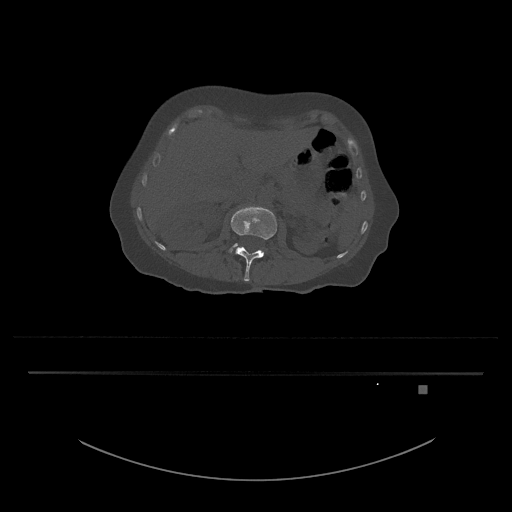
CT including the spine, one axial slice; slice 481 of 797 in the series (ordered by position); 120 kVp; bone window (W 1800 / L 400 HU); 0.5 mm slice thickness; 512 × 512 image matrix. Patient: female, 57 years. Case-level facts recorded for this patient, not image findings: primary cancer: cervical.
Structures marked on this image (semi-automatic segmentation, software-assisted and operator-edited):
- L3 vertebra: bounding box <229,243,238,253> (left, top, right, bottom; pixels)